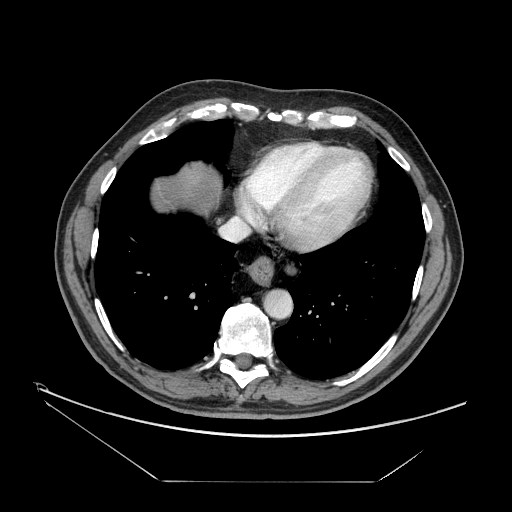
Contrast-enhanced abdominal CT, one axial slice; slice 153 of 161 in the series (ordered by position); reconstruction kernel STANDARD; 120 kVp; soft-tissue window (W 400 / L 40 HU); 2.5 mm slice thickness; 512 × 512 image matrix. Male patient, age 65 years. From the clinical record (not read from this slice): diagnosis: colorectal cancer liver metastases, imaged before liver resection; multiple liver metastases: yes; largest metastasis: 4.2 cm; disease in both lobes: yes.
Outlined on this slice (expert manual segmentation):
- hepatic veins: bounding box [x1, y1, x2, y2] px = [220, 162, 267, 241]
- liver: [150, 162, 220, 212]
- planned liver remnant (the part of the liver to remain after resection): [151, 162, 220, 213]